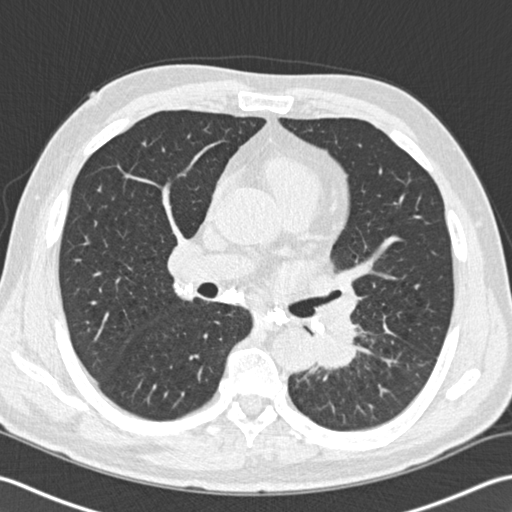
Low-dose screening chest CT, one axial slice. Reconstruction kernel B30f. 120 kVp. Lung window (W 1500 / L -600 HU). 512 × 512 image matrix, field of view 350 × 350 mm.
Structures marked on this image (outlined manually by an expert reader):
- lesion 1 (tumor, lower lobe of left lung): box from (x=317, y=314) to (x=356, y=369) px